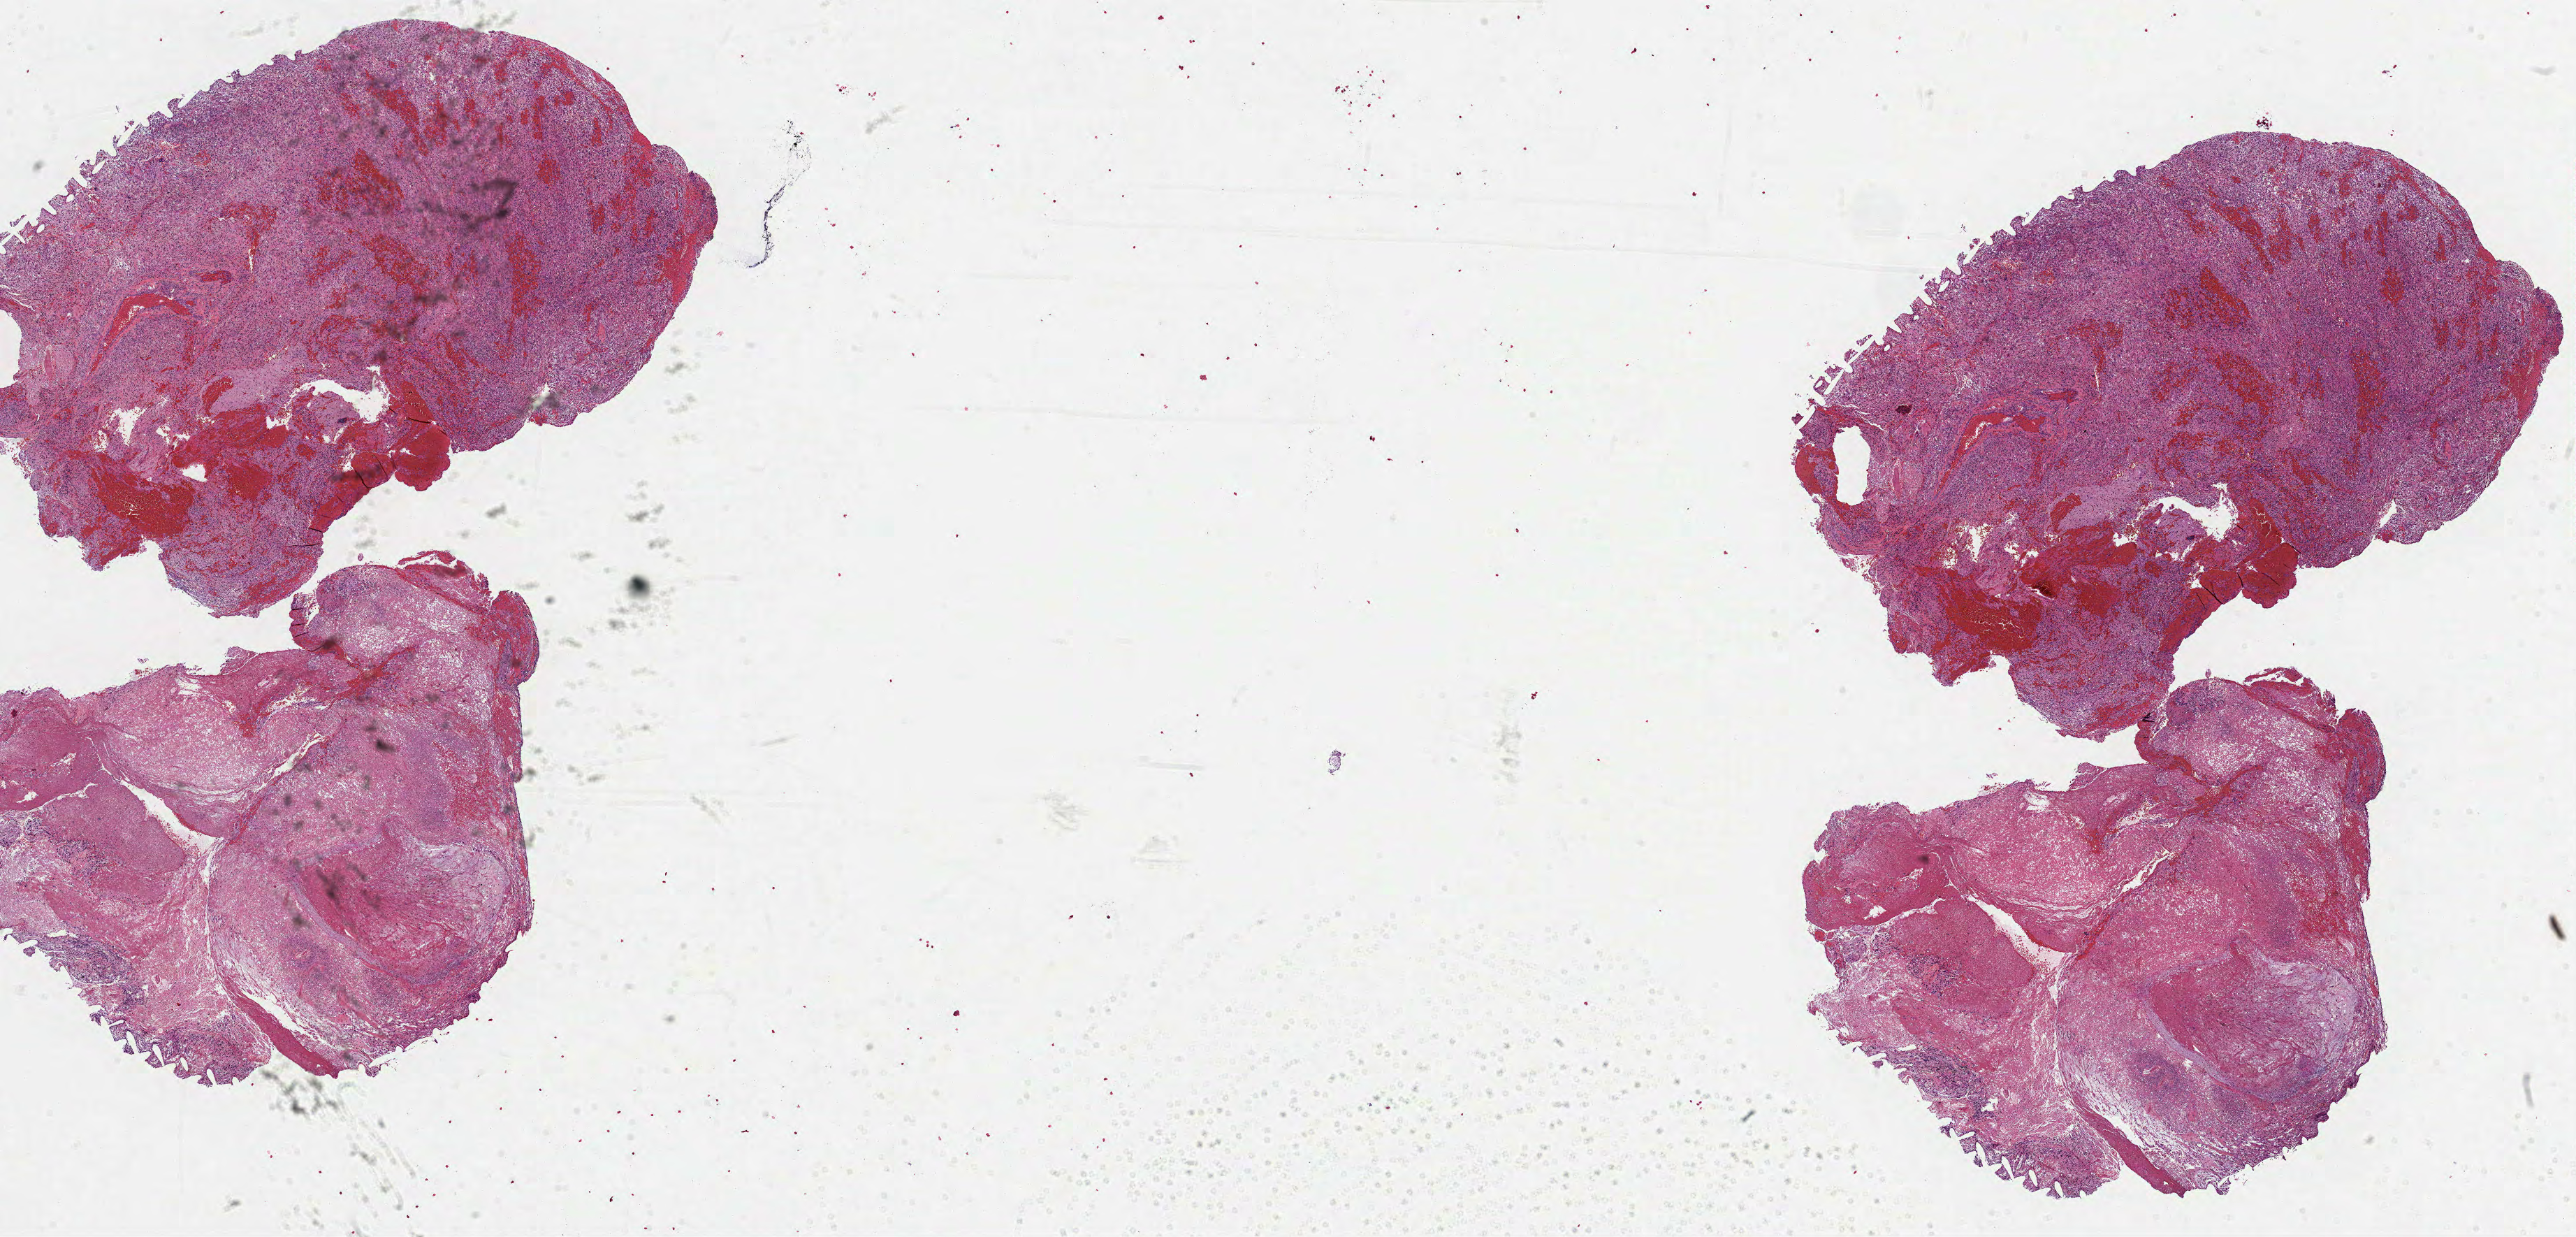
H&E-stained whole-slide image — low-resolution overview of the scanned area, about 29.7 x 14.3 mm (from a 40x scan); FFPE section; primary tumour sample from the brain. Patient: male, age at initial diagnosis 48 years.
Histologic diagnosis: Glioblastoma.